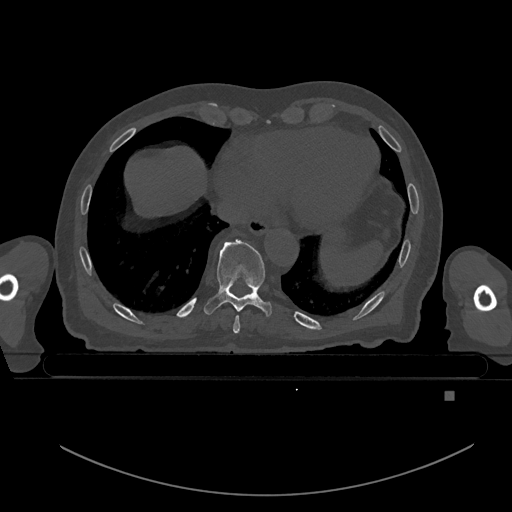
CT including the spine, one axial slice. Position 149 of 969 along the scan axis. Bone window (W 1800 / L 400 HU). 512 × 512 image matrix. Patient: male, 82 years. From the clinical record (not read from this slice): primary cancer: prostate; vertebrae with lytic lesions (as recorded): T11, T9, T8, T2.
Annotated regions visible in this slice (semi-automatically segmented with operator editing):
- T8 vertebra: bounding box (x1, y1, x2, y2) in pixels: (233, 315, 240, 333)
- T9 vertebra: (204, 240, 272, 317)